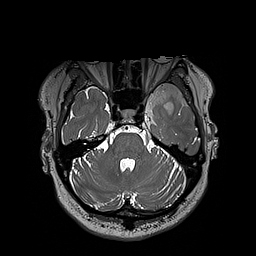
Brain MRI from a brain-tumour surgery series, one axial slice; position 144 of 192 along the scan axis; 256 × 256 image matrix. Case-level facts recorded for this patient, not image findings: histopathology: Oligodendroglioma; WHO grade: 3; IDH mutation: yes.
Outlined on this slice (outlined manually by an expert reader):
- tumour: bounding box [x1, y1, x2, y2] px = [153, 83, 193, 114]